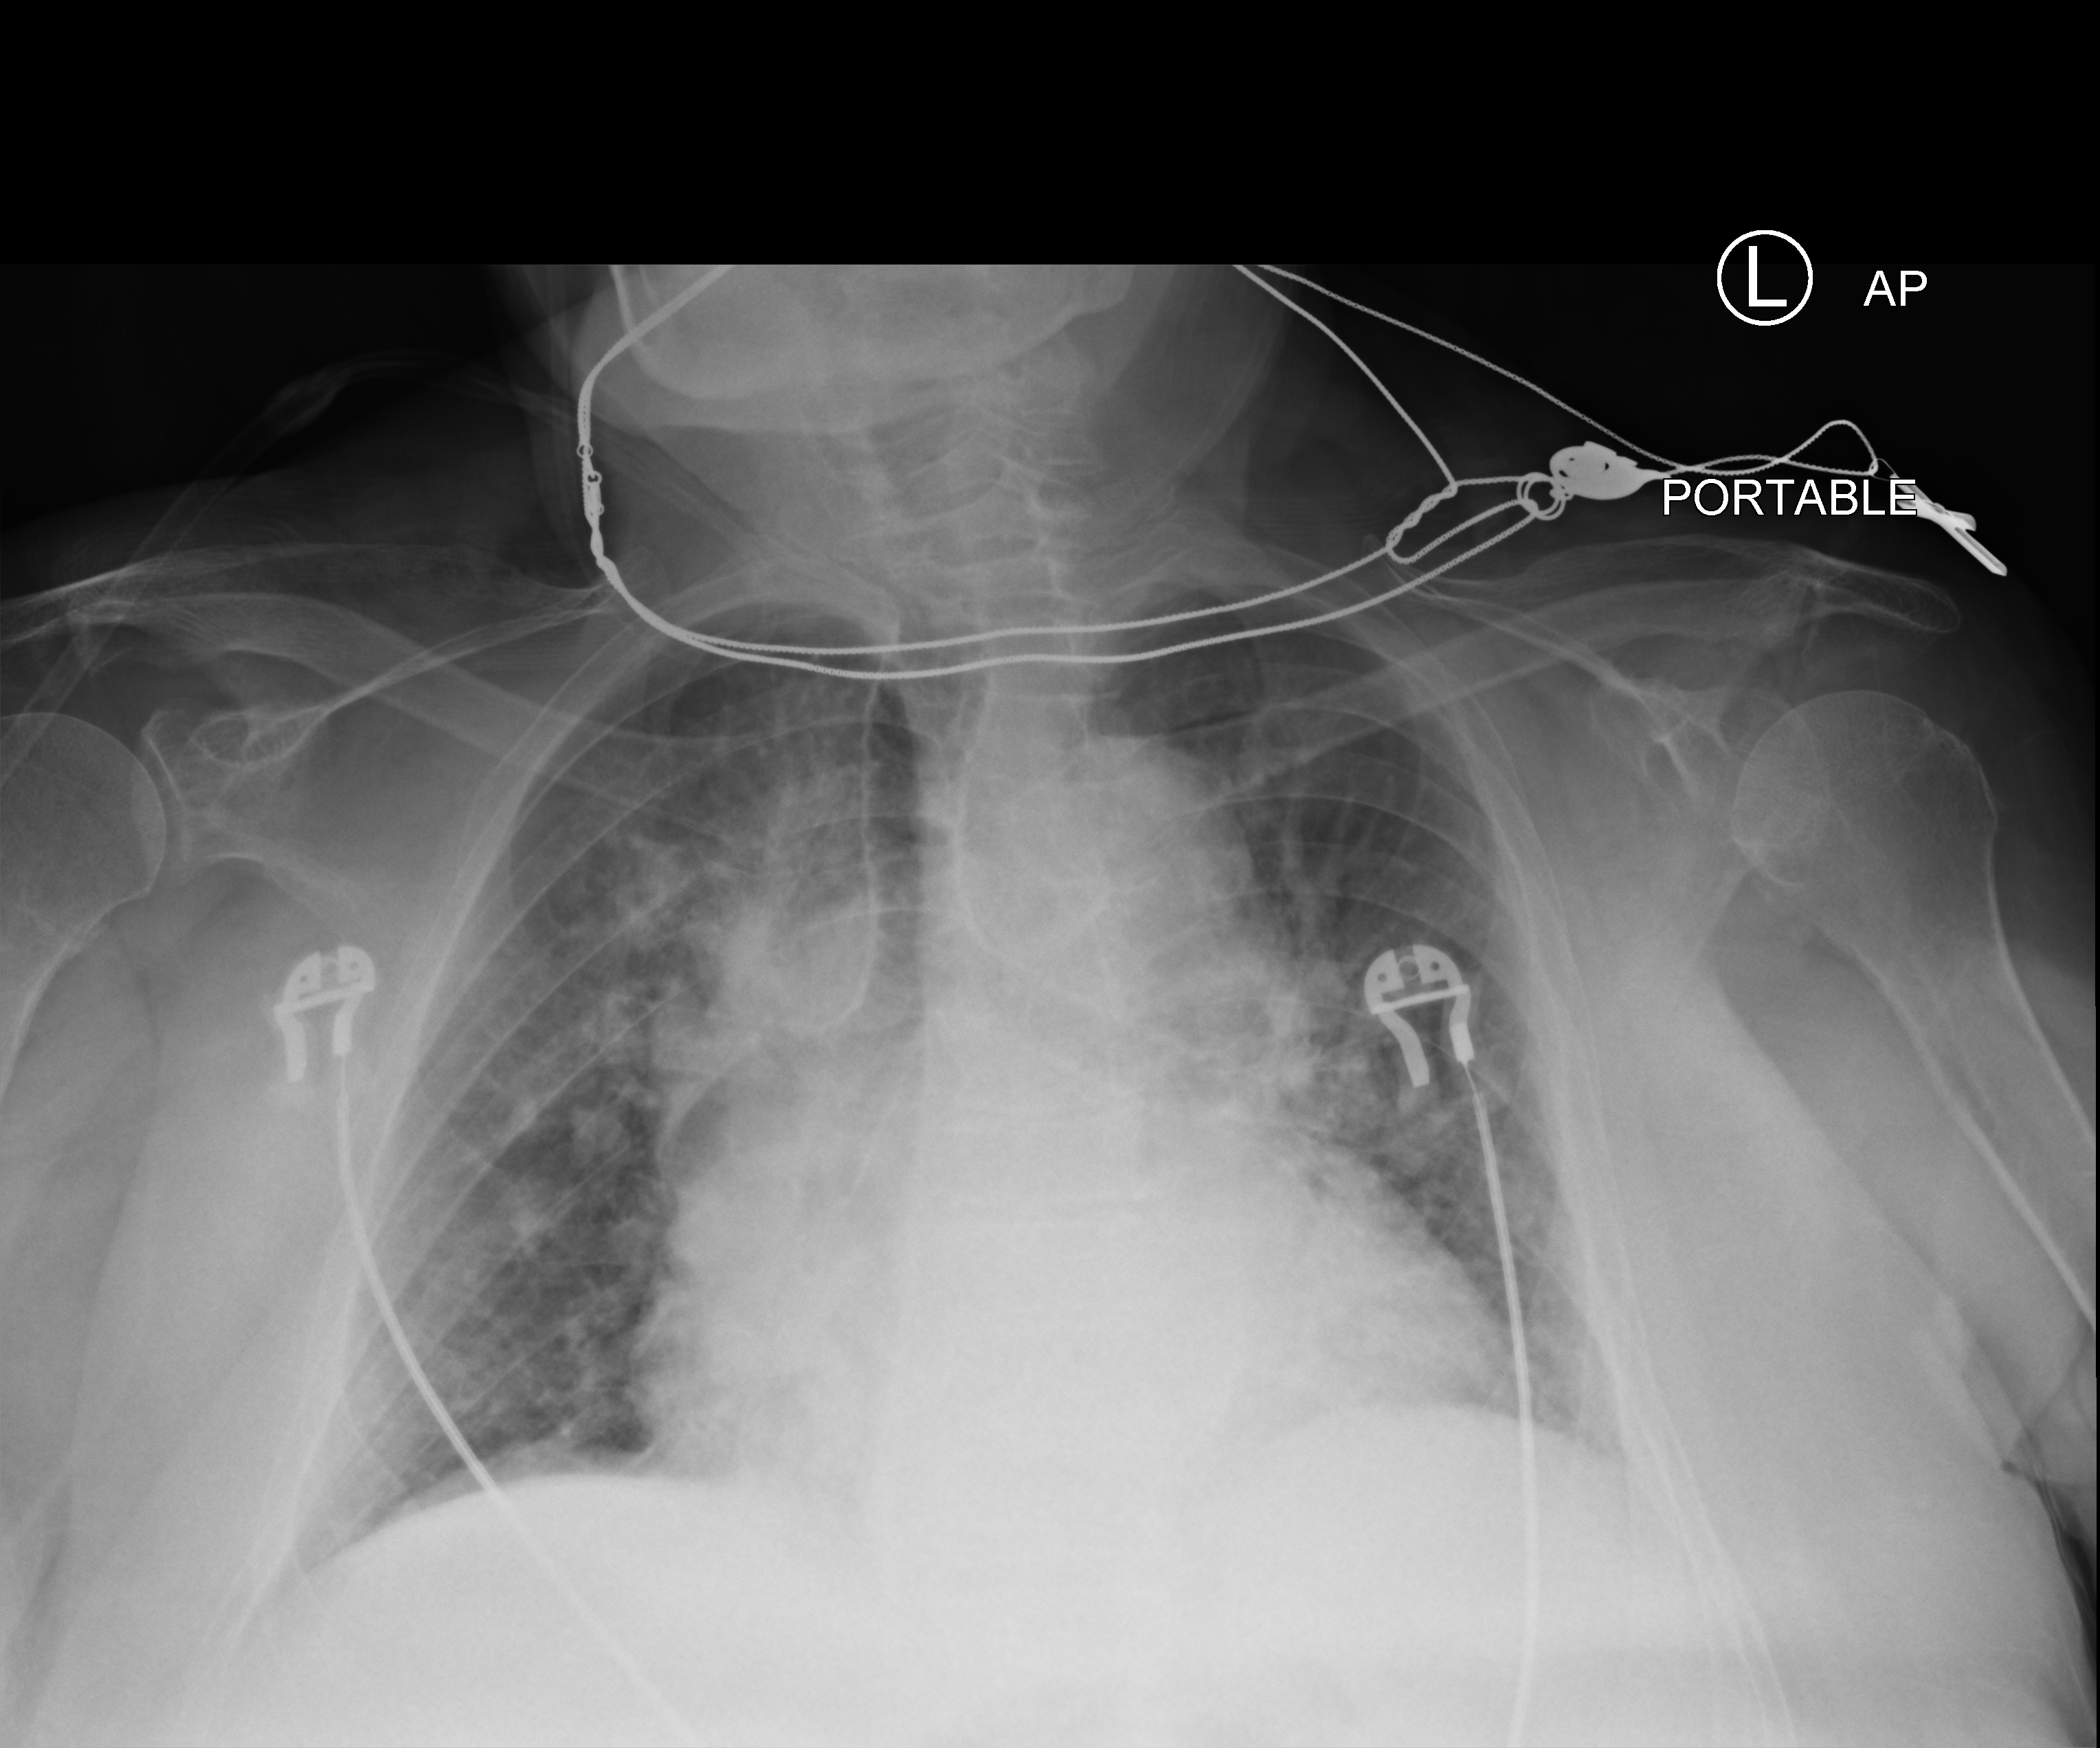
Chest X-ray (portable). Patient hospitalised with COVID-19; female, aged 75–90 years.
From the hospital-stay record, not from the radiograph (when in the stay this image was taken is not recorded): admitted to intensive care during this hospital stay: no.